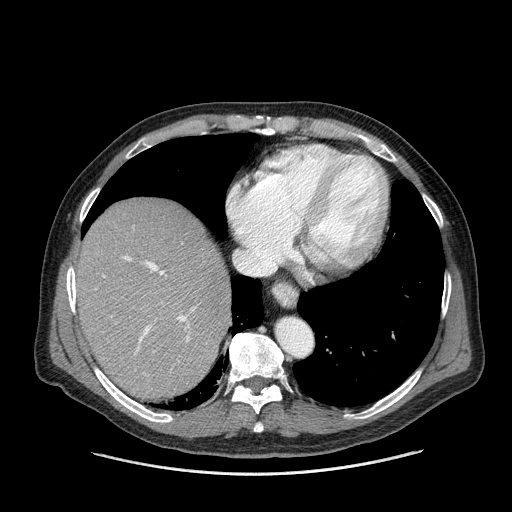
Contrast-enhanced abdominal CT (liver protocol), one axial slice. Position 128 of 180 along the scan axis. 120 kVp. One of 2 acquisitions stored at this slice position. Soft-tissue window (W 400 / L 40 HU). 512 × 512 image matrix, field of view 420 × 420 mm. Case-level facts recorded for this patient, not image findings: diagnosis: hepatocellular carcinoma (patient treated with transarterial chemoembolisation; whether this scan precedes or follows treatment is not stated here); TNM stage (as recorded): Stage-II; Child-Pugh class: A.
Annotated regions visible in this slice (semi-automatically segmented with operator editing):
- abdominal aorta: box from (x=276, y=319) to (x=312, y=356) px
- liver parenchyma outside the tumour (the mass and vessels are separate outlines, so this box may not span the whole liver): (x=78, y=198)–(x=230, y=398)
- liver vessels: (x=103, y=256)–(x=195, y=352)